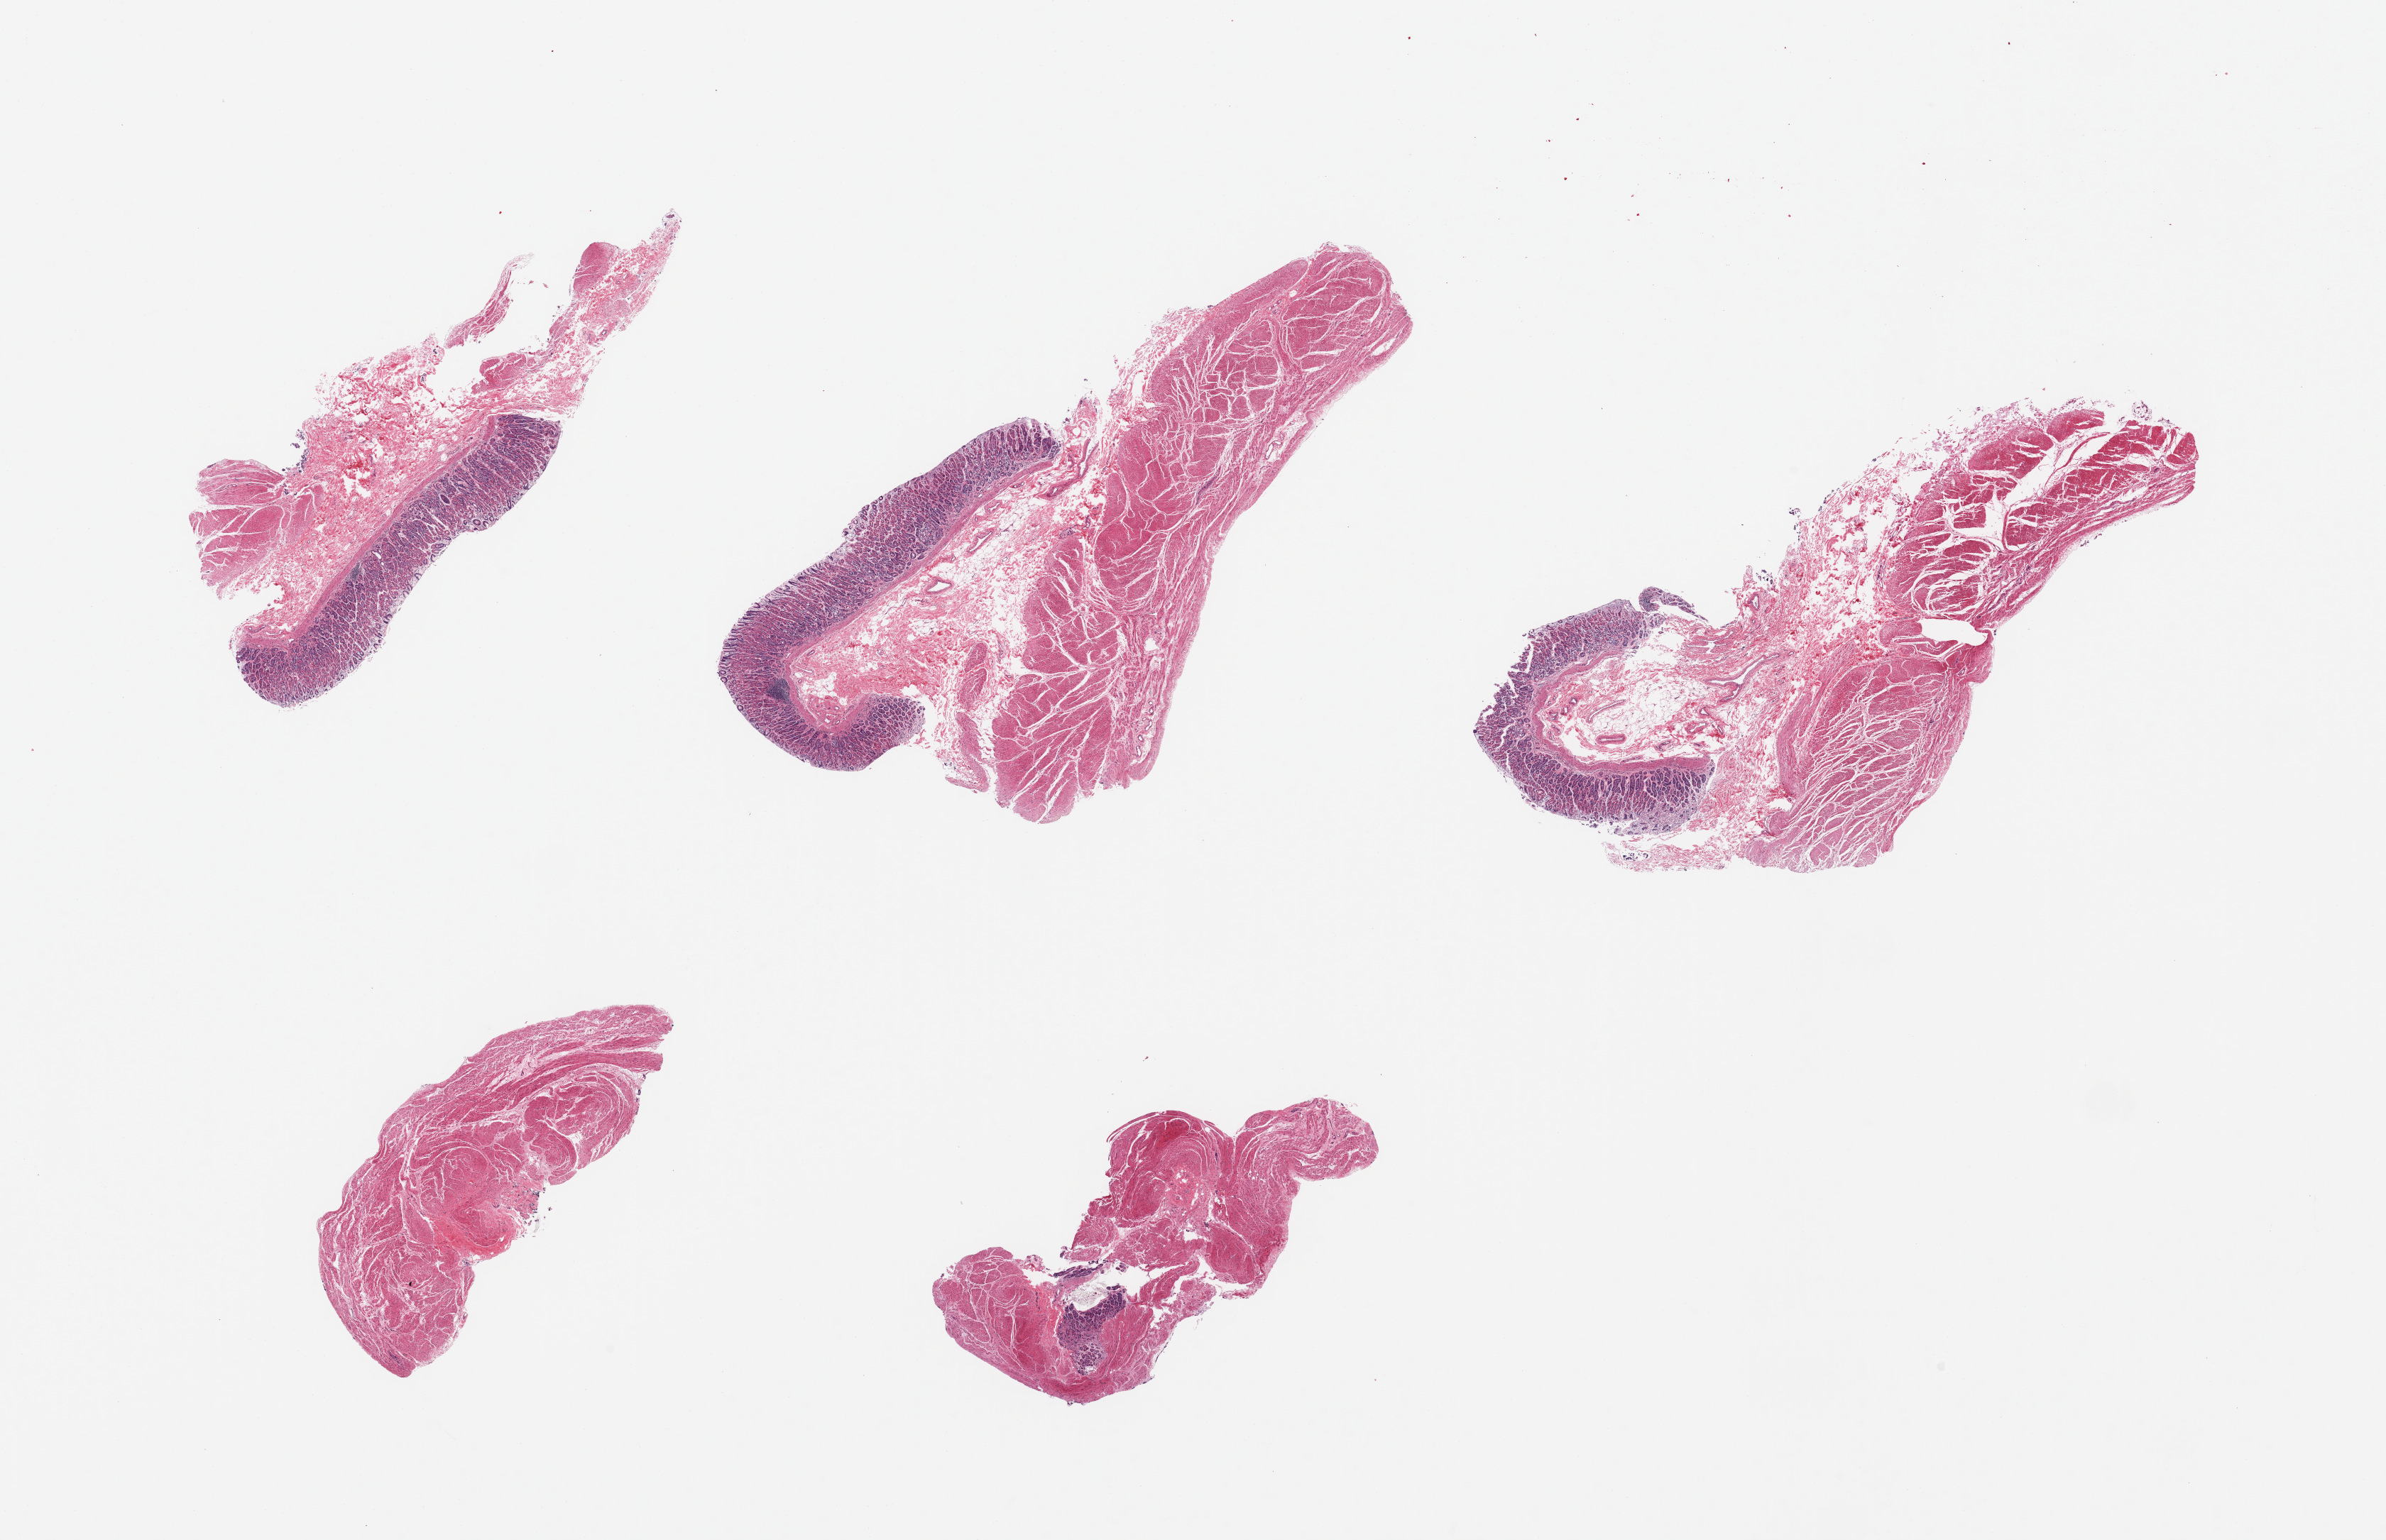
Whole-slide image, H&E stain, brightfield, low-resolution overview of the scanned area, about 26.6 x 17.2 mm. PAXgene-fixed paraffin-embedded (PFPE) section. Target tissue: stomach. Donor tissue sample.
* review note (as recorded): 5 pieces; 3 have mucosa and muscle, 2 have only muscle